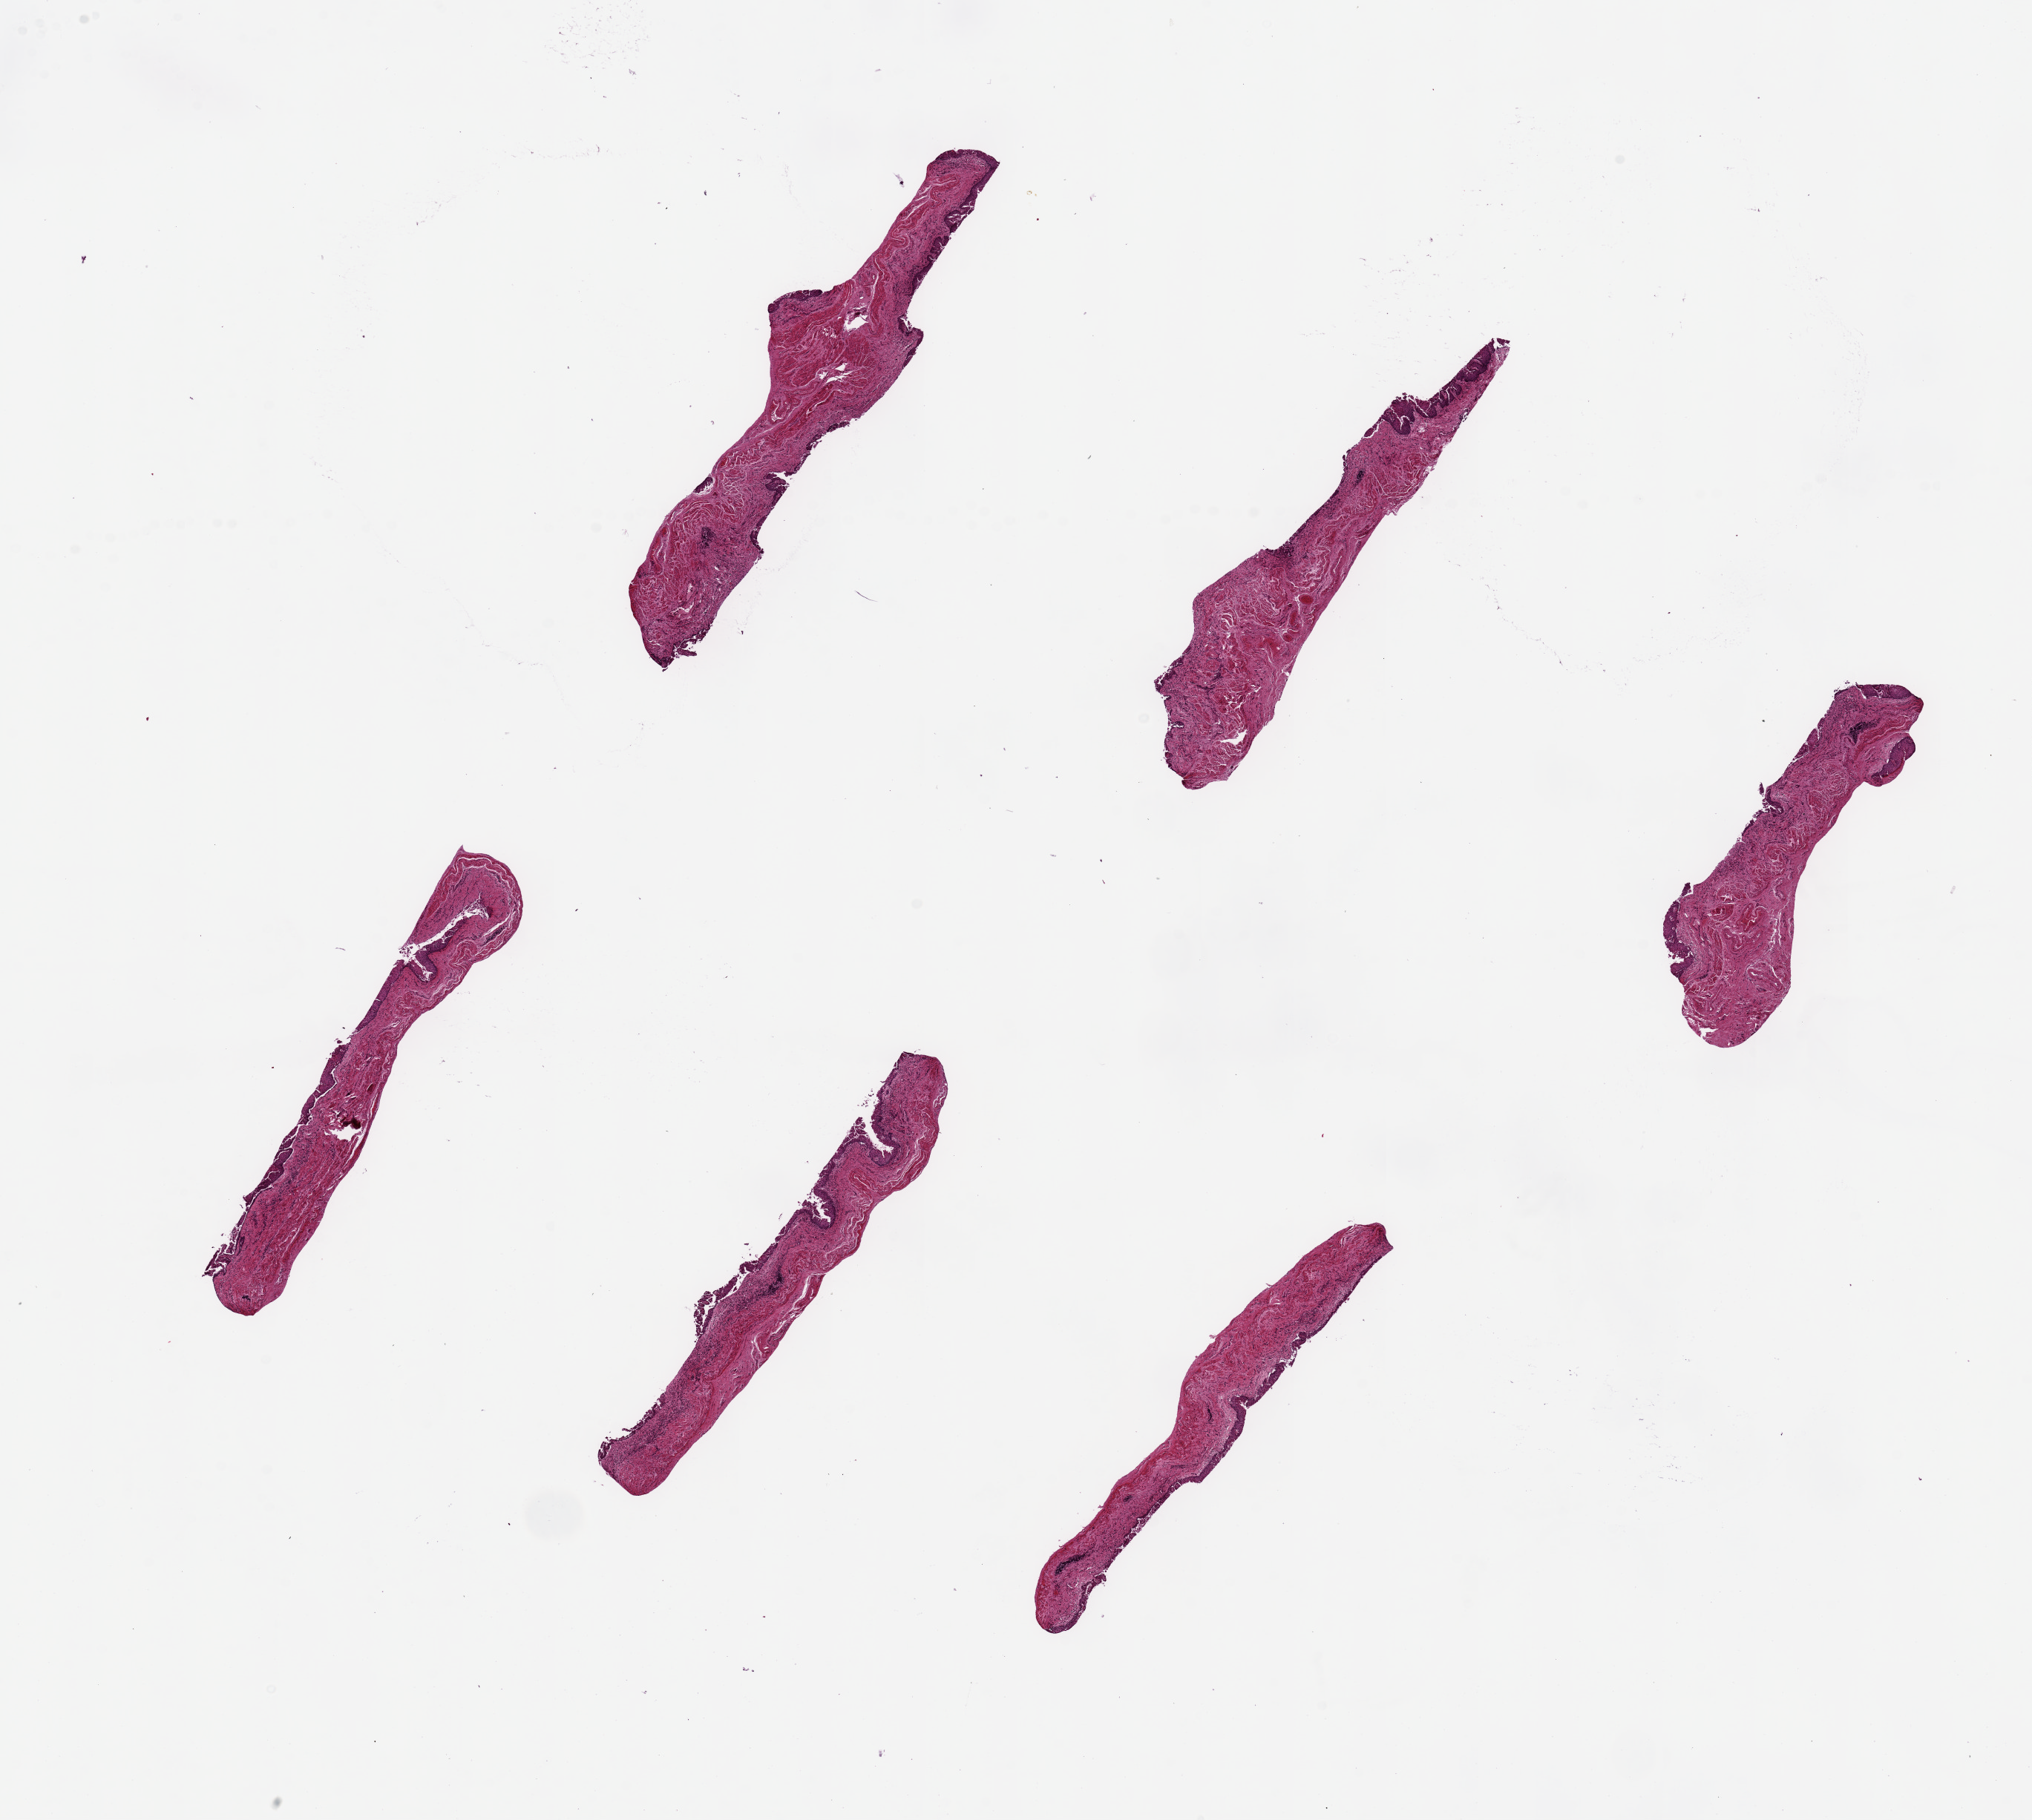
Digitized haematoxylin and eosin-stained section — shown as a low-resolution overview of the whole scanned area (about 21.7 x 19.4 mm); PAXgene-fixed paraffin-embedded (PFPE) section; target tissue: esophageal mucous membrane; donor tissue sample. Donor: male.
Pathologist's review note for this sample: 6 pieces, up to 6x1.5mm; partly sloughed epithelium.